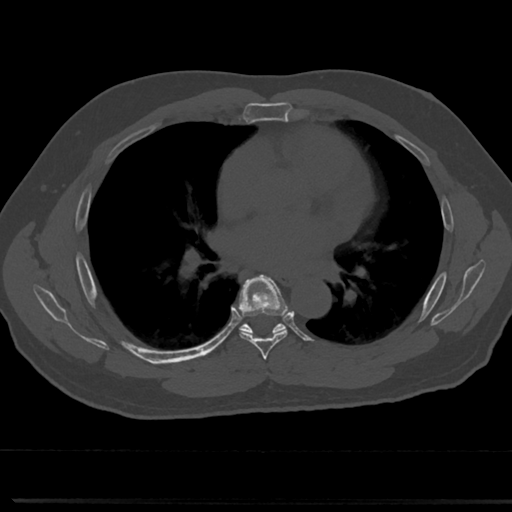
CT including the spine, one axial slice. Position 437 of 817 along the scan axis. Reconstruction kernel Br40s/3. 120 kVp. Bone window (W 1800 / L 400 HU). 0.5 mm slice thickness. 512 × 512 image matrix, field of view 355 × 355 mm. Male patient, age 61 years. From the clinical record (not read from this slice): primary cancer: prostate.
Annotated regions visible in this slice (semi-automatic segmentation, software-assisted and operator-edited):
- T5 vertebra: box from (x=264, y=369) to (x=273, y=377) px
- T6 vertebra: (x=232, y=277)–(x=308, y=351)
- T7 vertebra: (x=245, y=329)–(x=250, y=332)